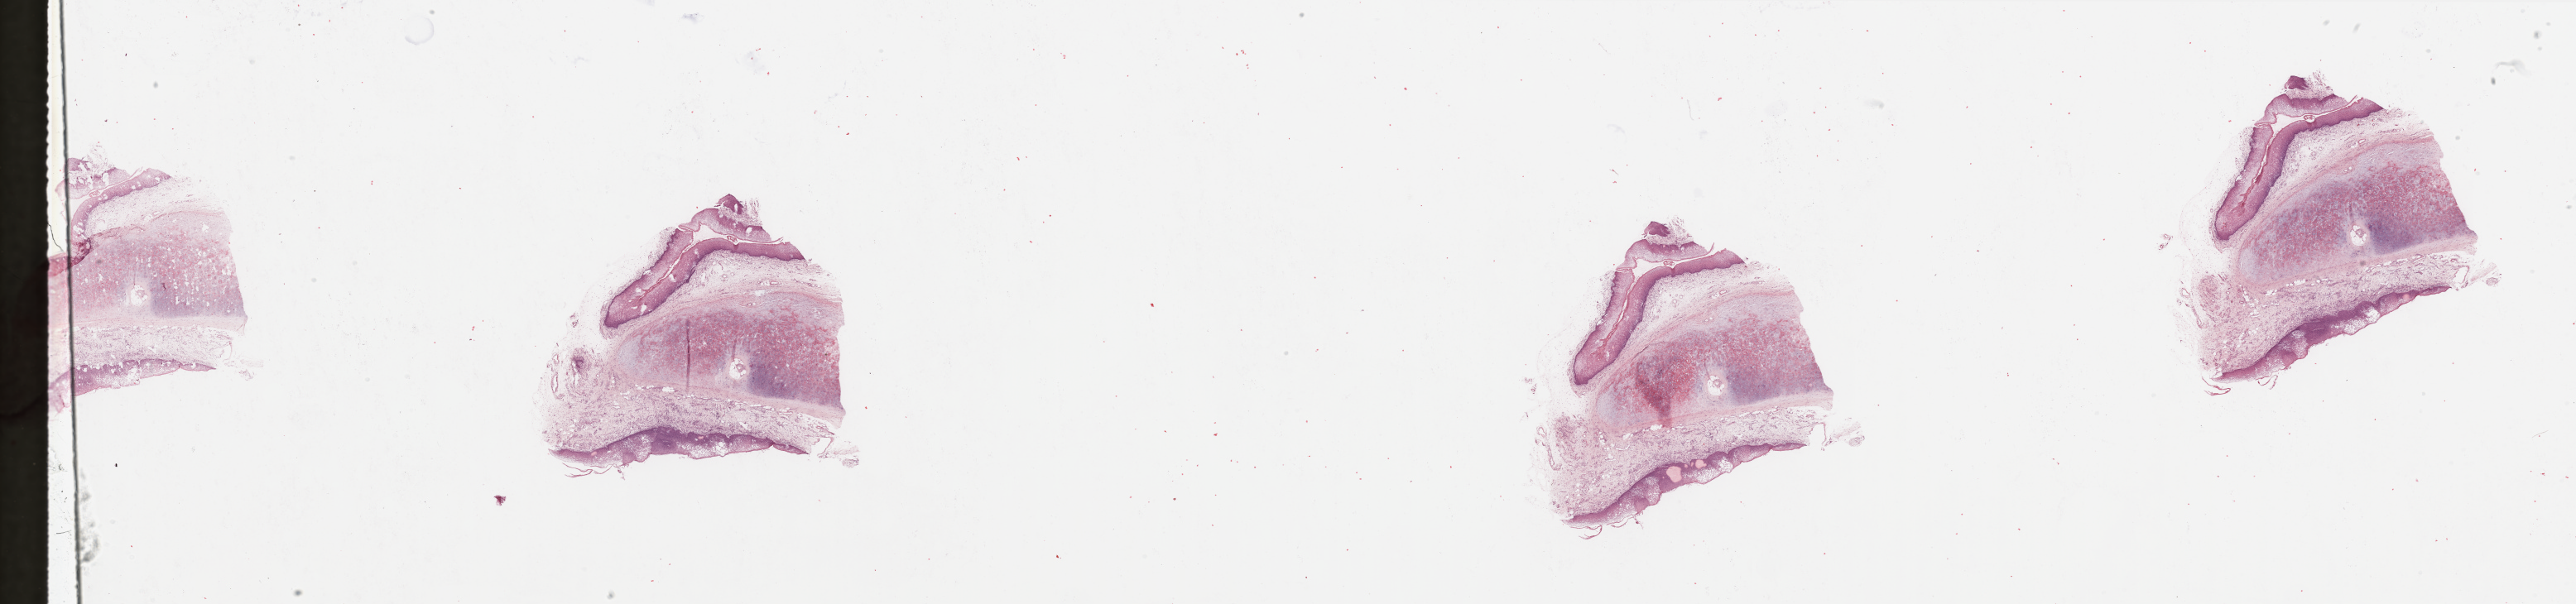
Whole-slide histology image, Hematoxylin and eosin (H&E) stained, a low-resolution overview of the entire scanned area, about 49.2 x 11.5 mm (acquisition: 20x scan). Normal (non-tumour) tissue sample, sampled site: larynx. Male, 71 y/o.
This section: normal (non-tumour) tissue from the same patient. Patient diagnosis: Squamous cell carcinoma, NOS (larynx, NOS).